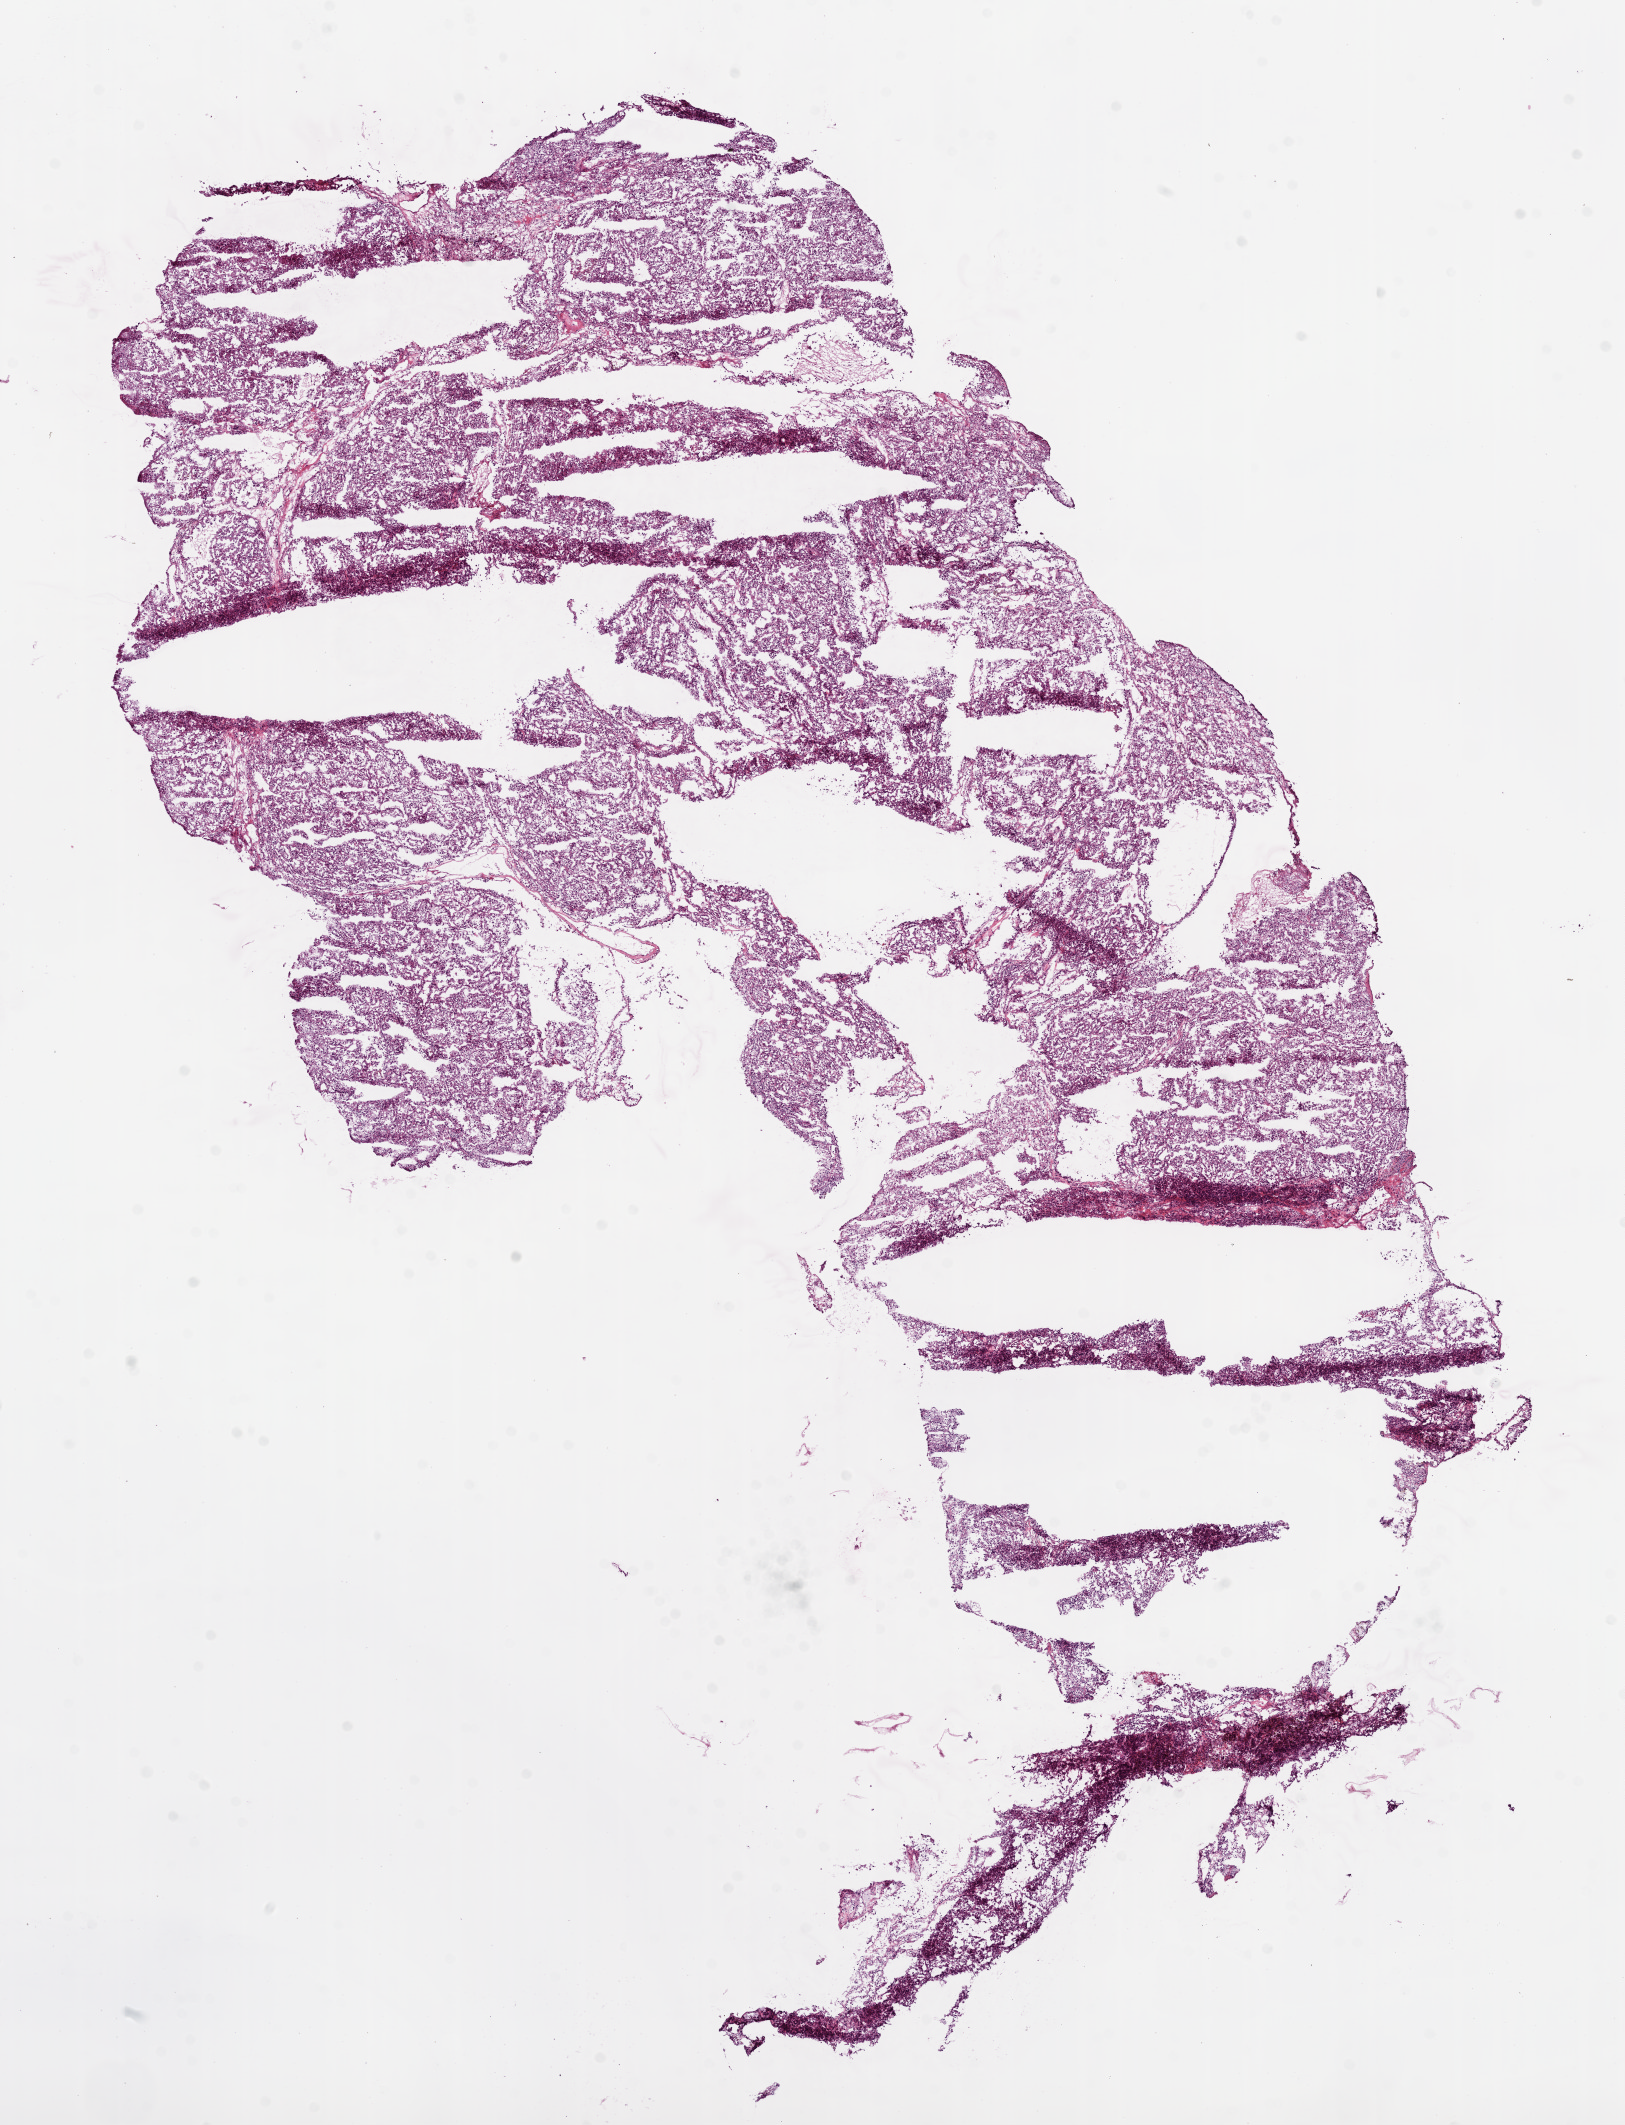
H&E whole-slide image, low-resolution overview of the scanned area, about 13.0 x 17.1 mm. Frozen section. Sample: primary tumour, kidney. Patient: female, age at initial diagnosis 79 years. Histologic grade: G3 (poorly differentiated). Composition of this section per pathologist review: tumour cells 90%, tumour nuclei 85%, normal cells 0%, stromal cells 10%, necrosis 0%.
- histologic diagnosis: Clear cell adenocarcinoma, NOS
- TNM: T1 NX M0
- AJCC pathologic stage: I